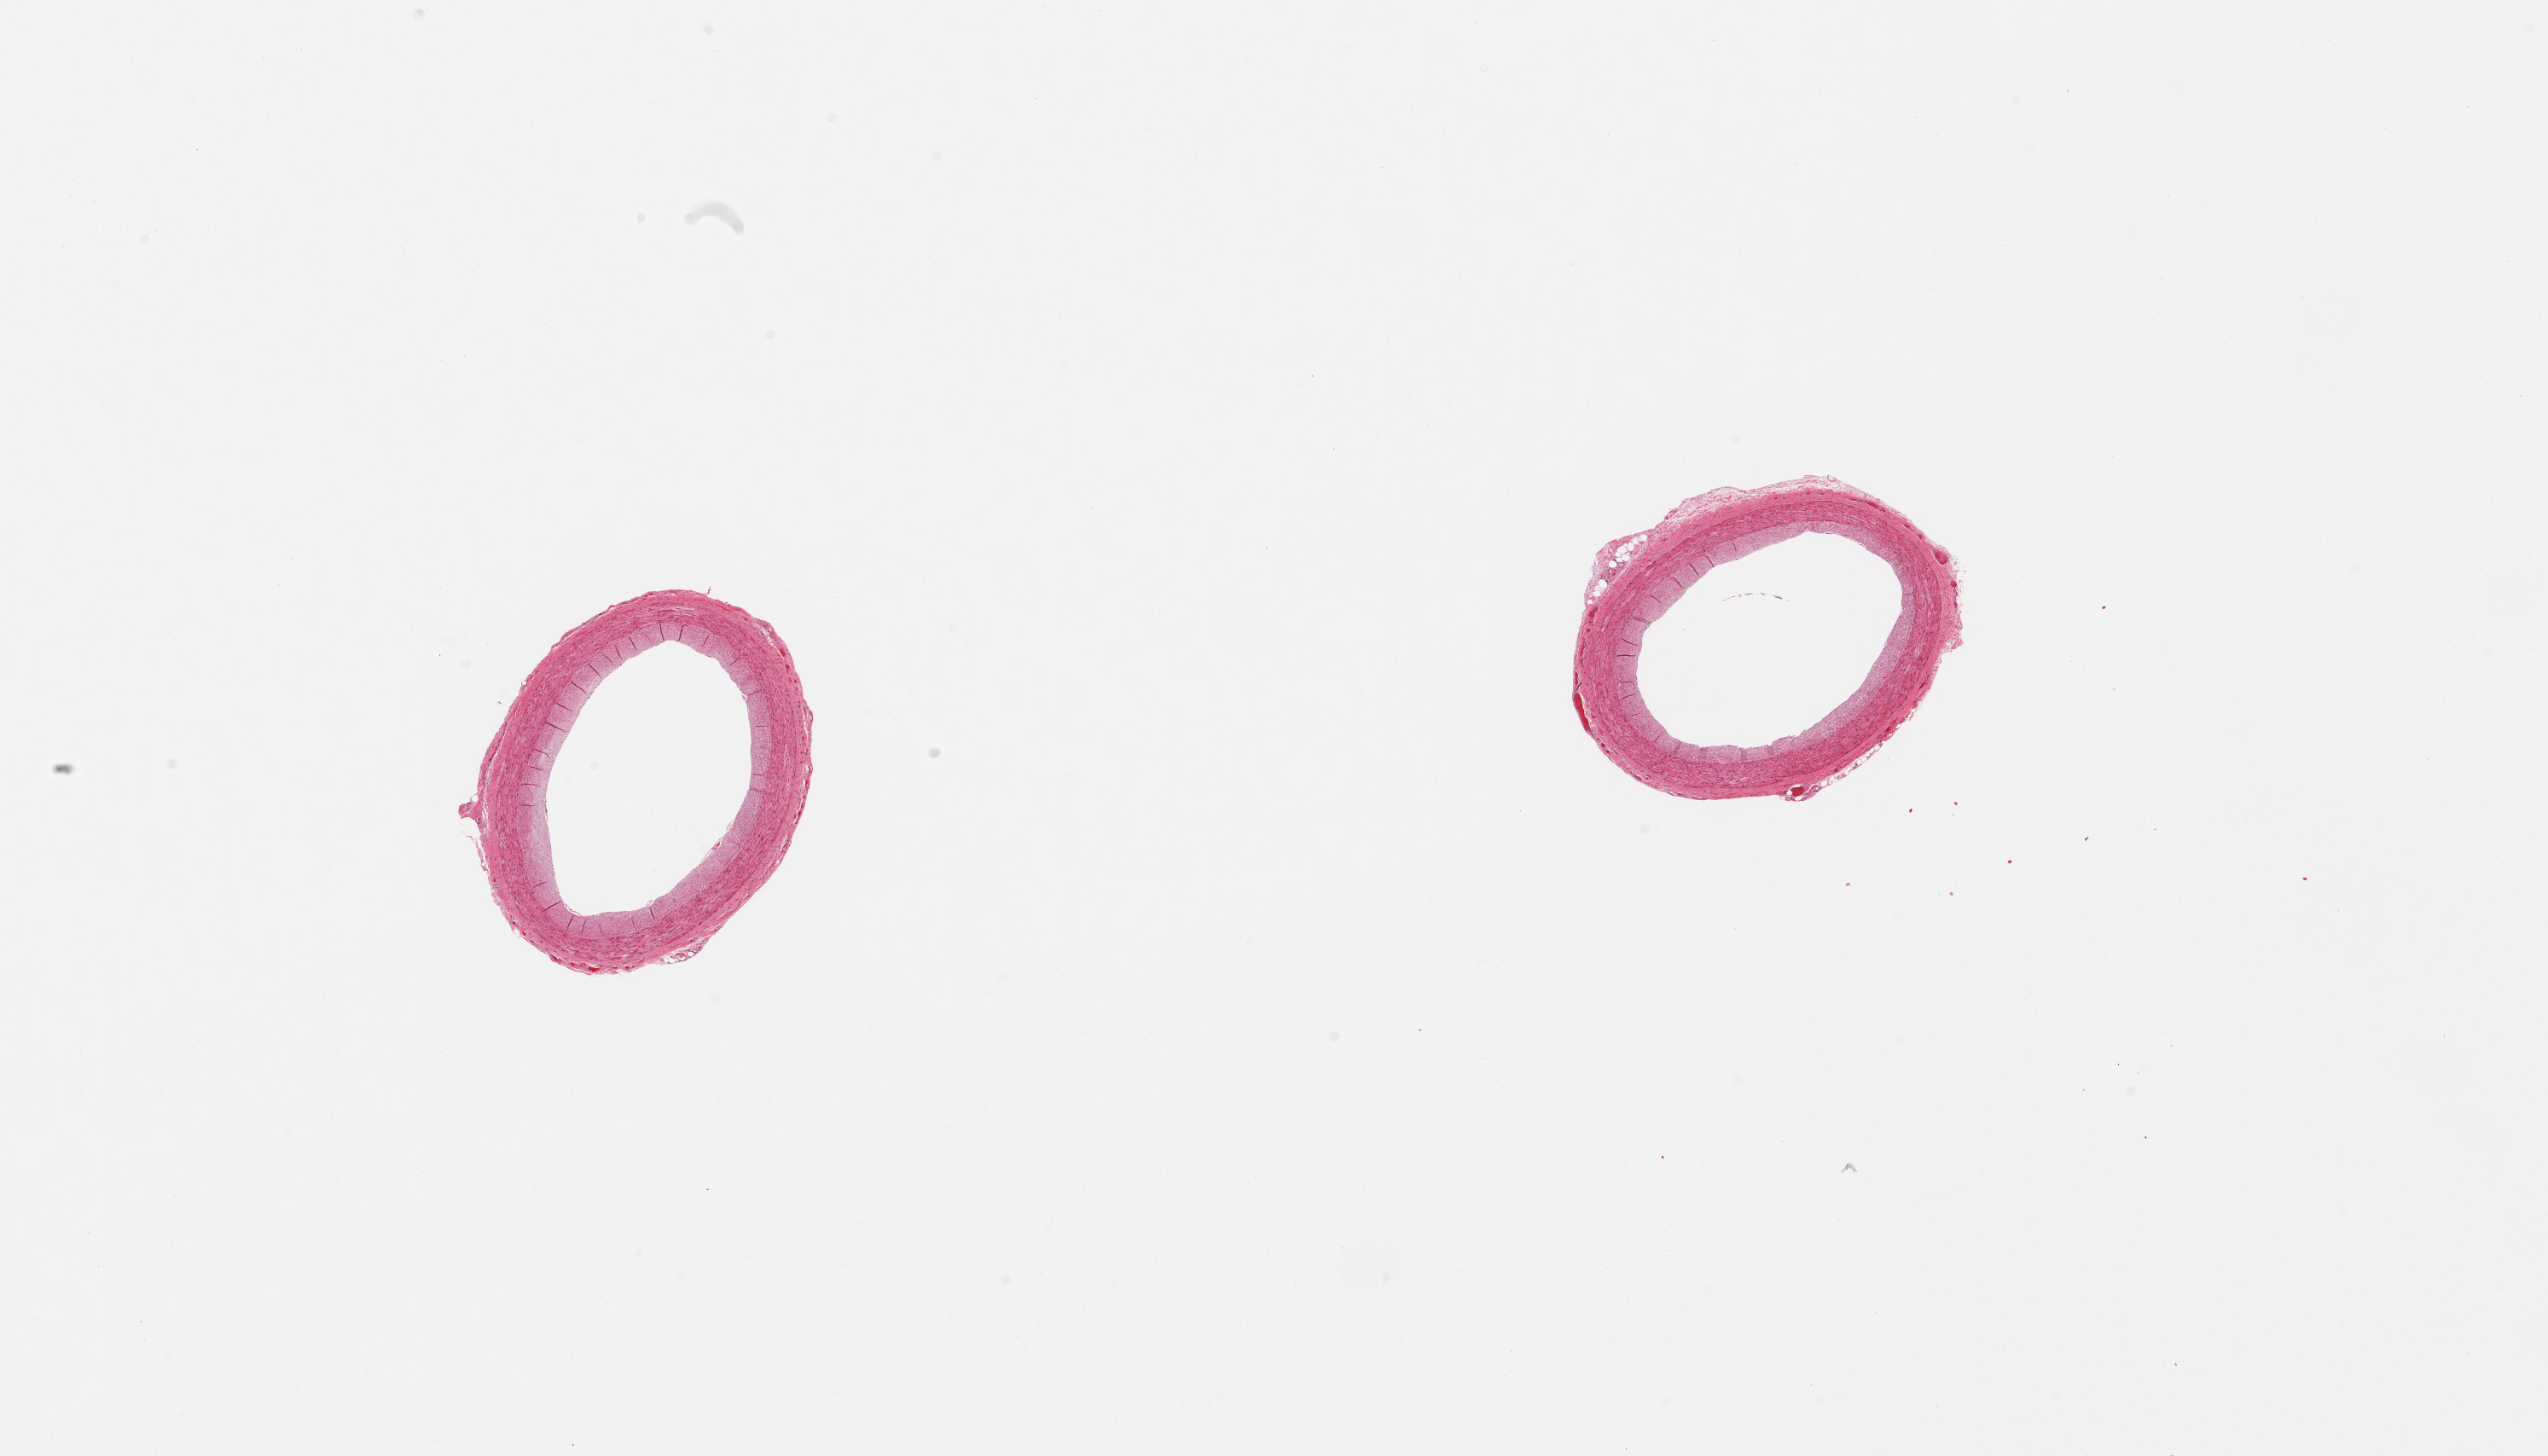
Whole-slide image, haematoxylin and eosin stain, brightfield — shown as a low-resolution overview of the whole scanned area (about 23.6 x 13.5 mm). PAXgene-fixed, paraffin-embedded tissue. Target tissue: coronary artery. Donor tissue sample. Male donor.
* pathologist's review note for this sample: 2 pieces, no atherosis